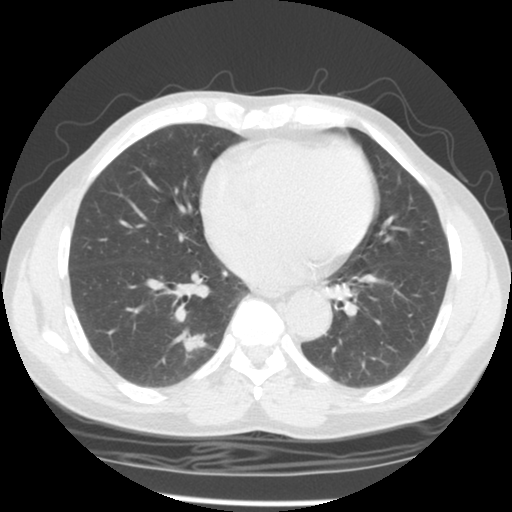
Low-dose screening chest CT, one axial slice; position 56 of 127 along the scan axis; 140 kVp; lung window (W 1500 / L -600 HU); 2.5 mm slice thickness; 512 × 512 image matrix, field of view 320 × 320 mm.
Annotated regions visible in this slice (outlined manually by an expert reader):
- lesion 1 (tumor, lower lobe of right lung): bounding box <174,328,206,351> (left, top, right, bottom; pixels)